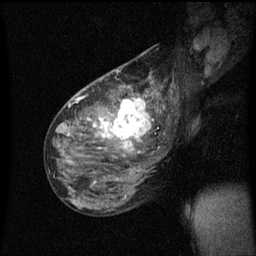
Breast MRI (dynamic contrast-enhanced), one sagittal slice; position 32 of 60 along the scan axis; dynamic contrast-enhanced series, image 2 of 3 at this slice position (ordered by acquisition); 1.5 T; TE 4.2 ms, TR 8.4 ms; 2 mm slice thickness; 256 × 256 image matrix. Female patient, age 49 years.
Structures marked on this image (semi-automatically segmented with operator editing):
- analysis volume of interest (the breast-tissue region the enhancement analysis was run in; not a lesion): bounding box (x1, y1, x2, y2) in pixels: (103, 90, 157, 151)
- tumour enhancement mask (voxels above the 70 % enhancement threshold inside the analysis volume of interest): (103, 96, 152, 151)